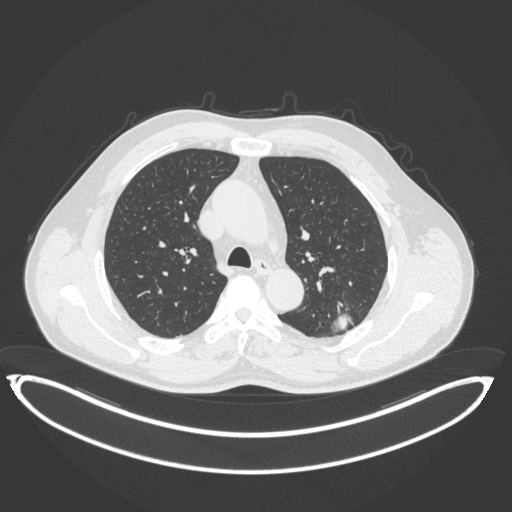
Chest CT, one axial slice; slice 248 of 399 in the series (ordered by position); reconstruction kernel B31f; 120 kVp; lung window (W 1500 / L -600 HU); 512 × 512 image matrix. Male patient, age 58 years. From the clinical record (not read from this slice): clinical TNM (as recorded): T1c N0 M0.
Outlined on this slice (bounding box drawn by a radiologist):
- lung tumour (recorded histology: adenocarcinoma): box from (x=326, y=304) to (x=356, y=335) px